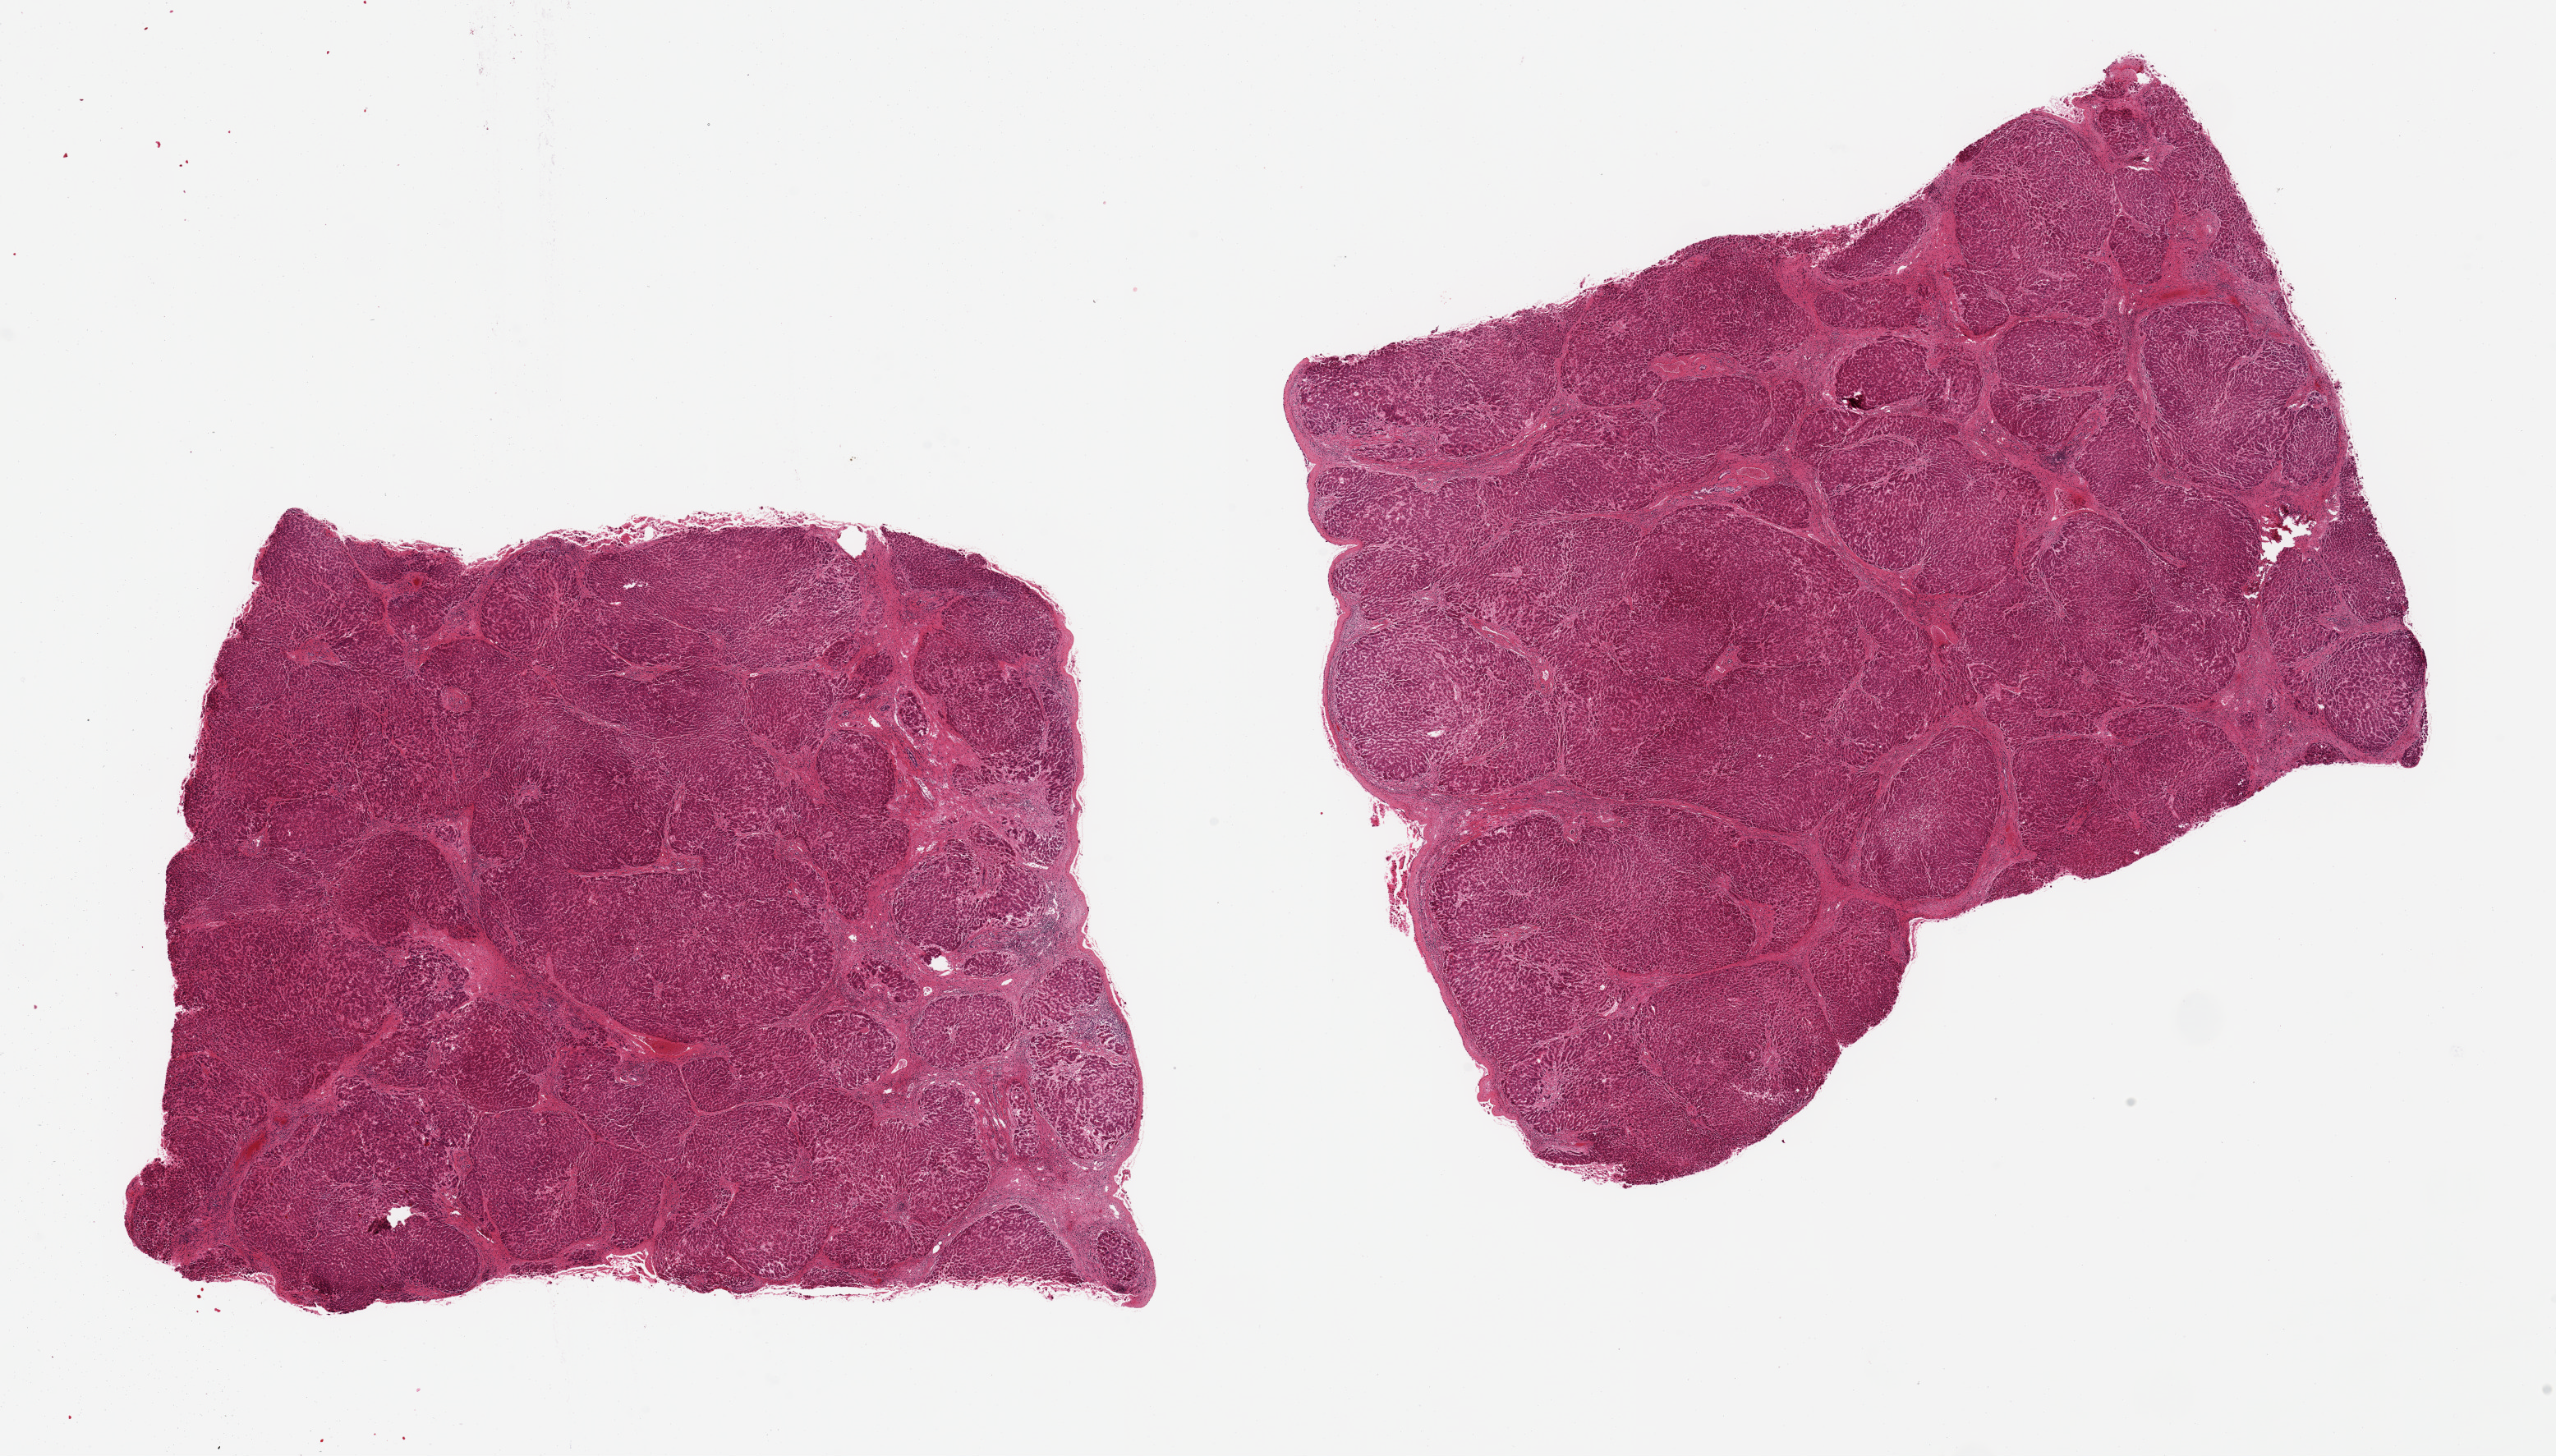
Whole-slide image, hematoxylin and eosin (H&E) stain, whole scanned area (about 24.6 x 14.0 mm, acquisition: 20x scan) shown as a low-resolution overview, PAXgene-fixed, paraffin-embedded tissue, section of liver (target tissue), donor tissue sample. Donor sex: female.
* reviewer comment on this tissue sample: 2 pieces, 10x8 & 9x7 mm; cirrhosis, microsteatosis; capsule present